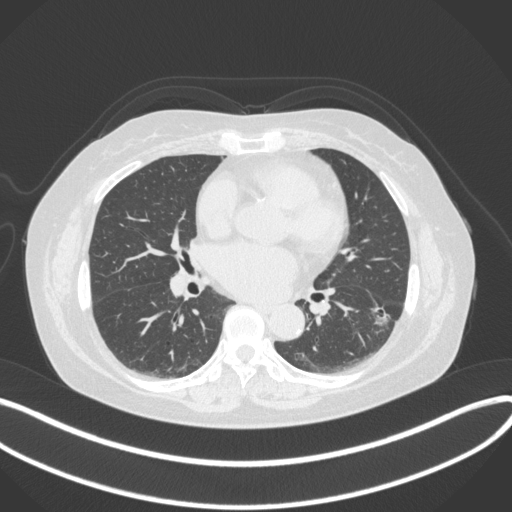
Chest CT, one axial slice; slice 173 of 373 in the series (ordered by position); reconstruction kernel B31f; lung window (W 1500 / L -600 HU); 512 × 512 image matrix, field of view 400 × 400 mm. Female patient, age 67 years. Case-level facts recorded for this patient, not image findings: clinical TNM (as recorded): T1c N0 M0; histopathological grade: G2.
Annotated regions visible in this slice (bounding box drawn by a radiologist):
- lung tumour (recorded histology: adenocarcinoma): box from (x=363, y=300) to (x=395, y=332) px